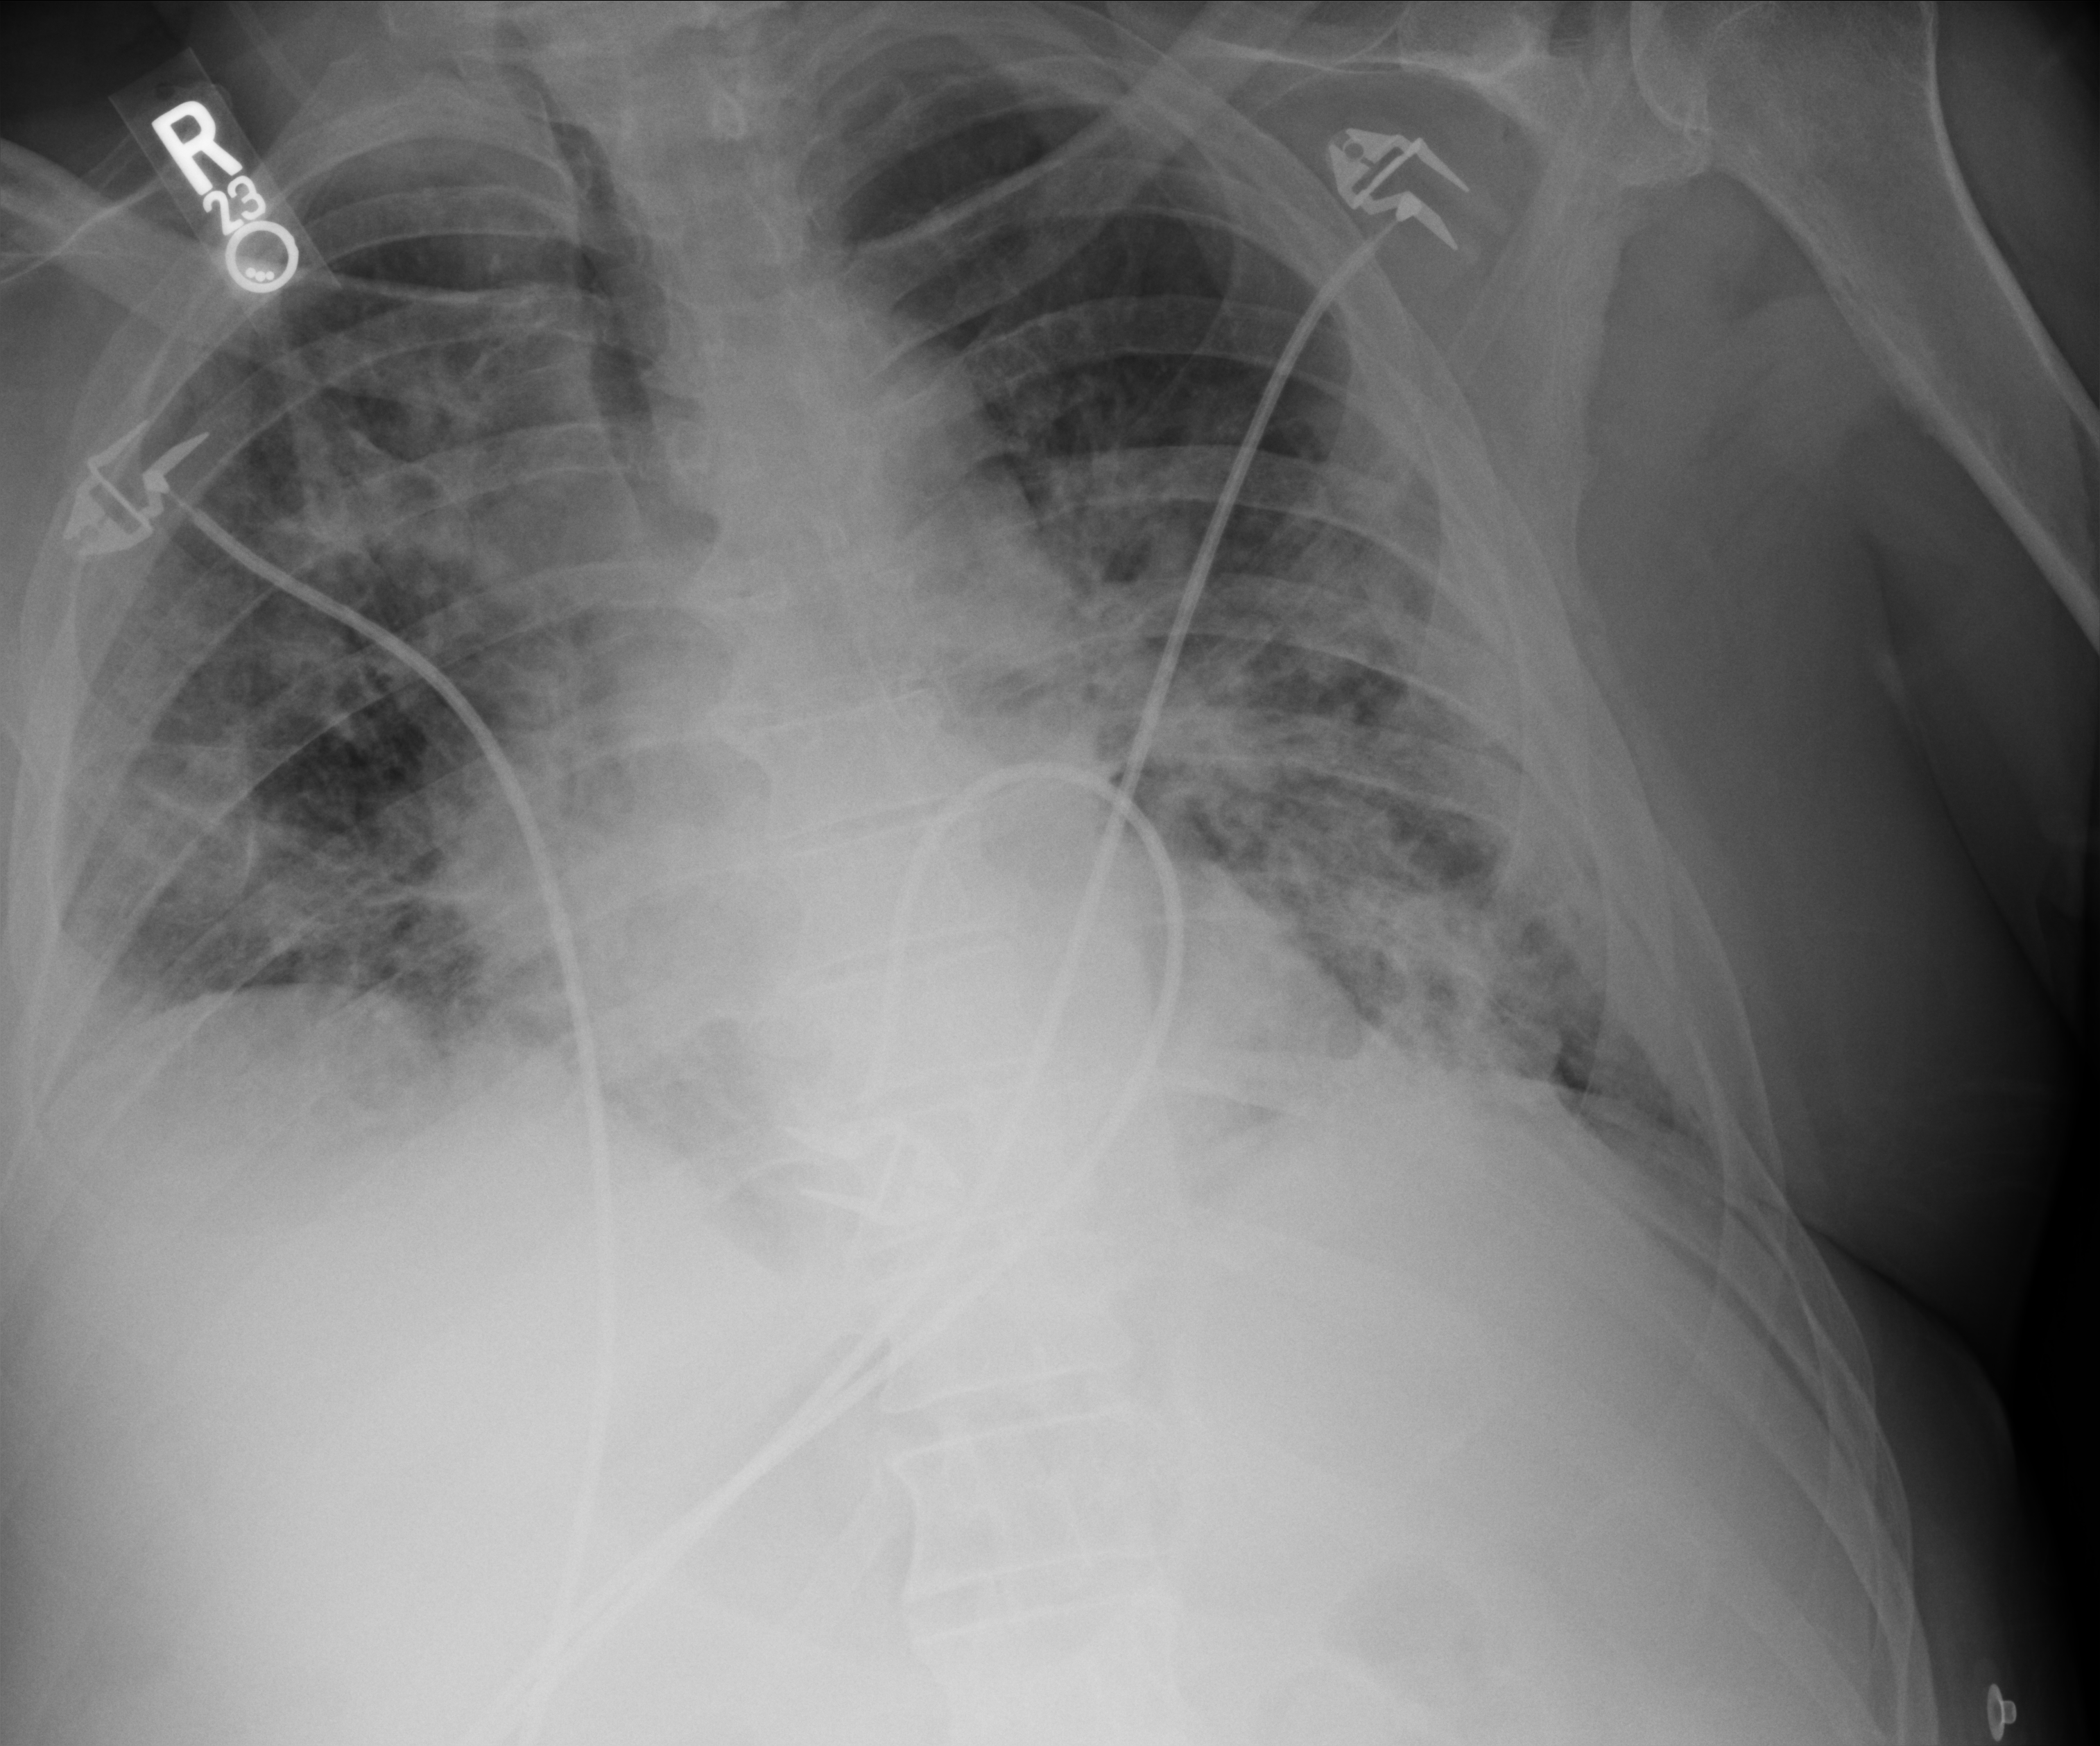
Bedside chest radiograph (computed radiography). Male patient hospitalised with COVID-19, age 60–74 years.
From the hospital-stay record, not from the radiograph (when in the stay this image was taken is not recorded):
- mechanically ventilated during this hospital stay: no
- length of hospital stay: 9 days